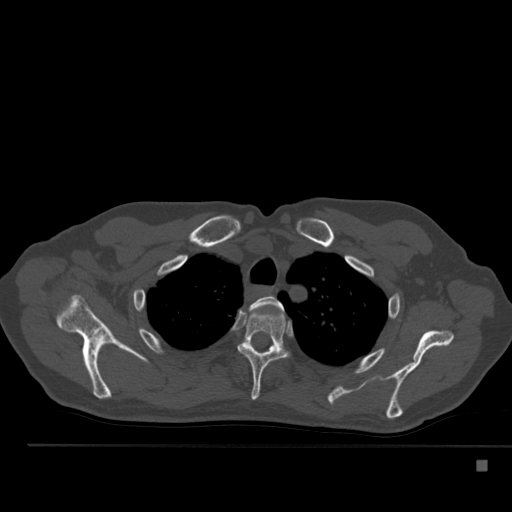
CT including the spine, one axial slice. Slice 397 of 517 in the series (ordered by position). Reconstruction kernel Br40s. 120 kVp. Bone window (W 1800 / L 400 HU). 1.5 mm slice thickness. 512 × 512 image matrix. Male patient, age 70 years. Case-level facts recorded for this patient, not image findings: primary cancer: renal.
Annotated regions visible in this slice (semi-automatic segmentation, software-assisted and operator-edited):
- T2 vertebra: bounding box <250,296,283,309> (left, top, right, bottom; pixels)
- T3 vertebra: <237,311,287,400>
- T4 vertebra: <269,345,275,351>